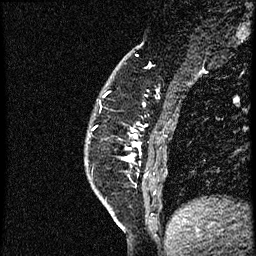
Breast MRI (dynamic contrast-enhanced), one sagittal slice; slice 15 of 56 in the series (ordered by position); dynamic contrast-enhanced study with each time point stored as its own series, time point 2 of 4 at this slice position (early post-contrast, ordered by acquisition time); 1.5 T; TE 4.2 ms, TR 18.9 ms; 2 mm slice thickness; 256 × 256 image matrix, field of view 200 × 200 mm. Female patient. From the clinical record (not read from this slice): setting: breast cancer imaged before/during neoadjuvant chemotherapy; receptor status: HER2-positive.
Outlined on this slice (semi-automatically segmented with operator editing):
- analysis volume of interest (the breast-tissue region the enhancement analysis was run in; not a lesion): box from (x=125, y=86) to (x=174, y=189) px
- tumour enhancement mask (voxels above the 100 % enhancement threshold inside the analysis volume of interest): (x=125, y=130)–(x=142, y=160)